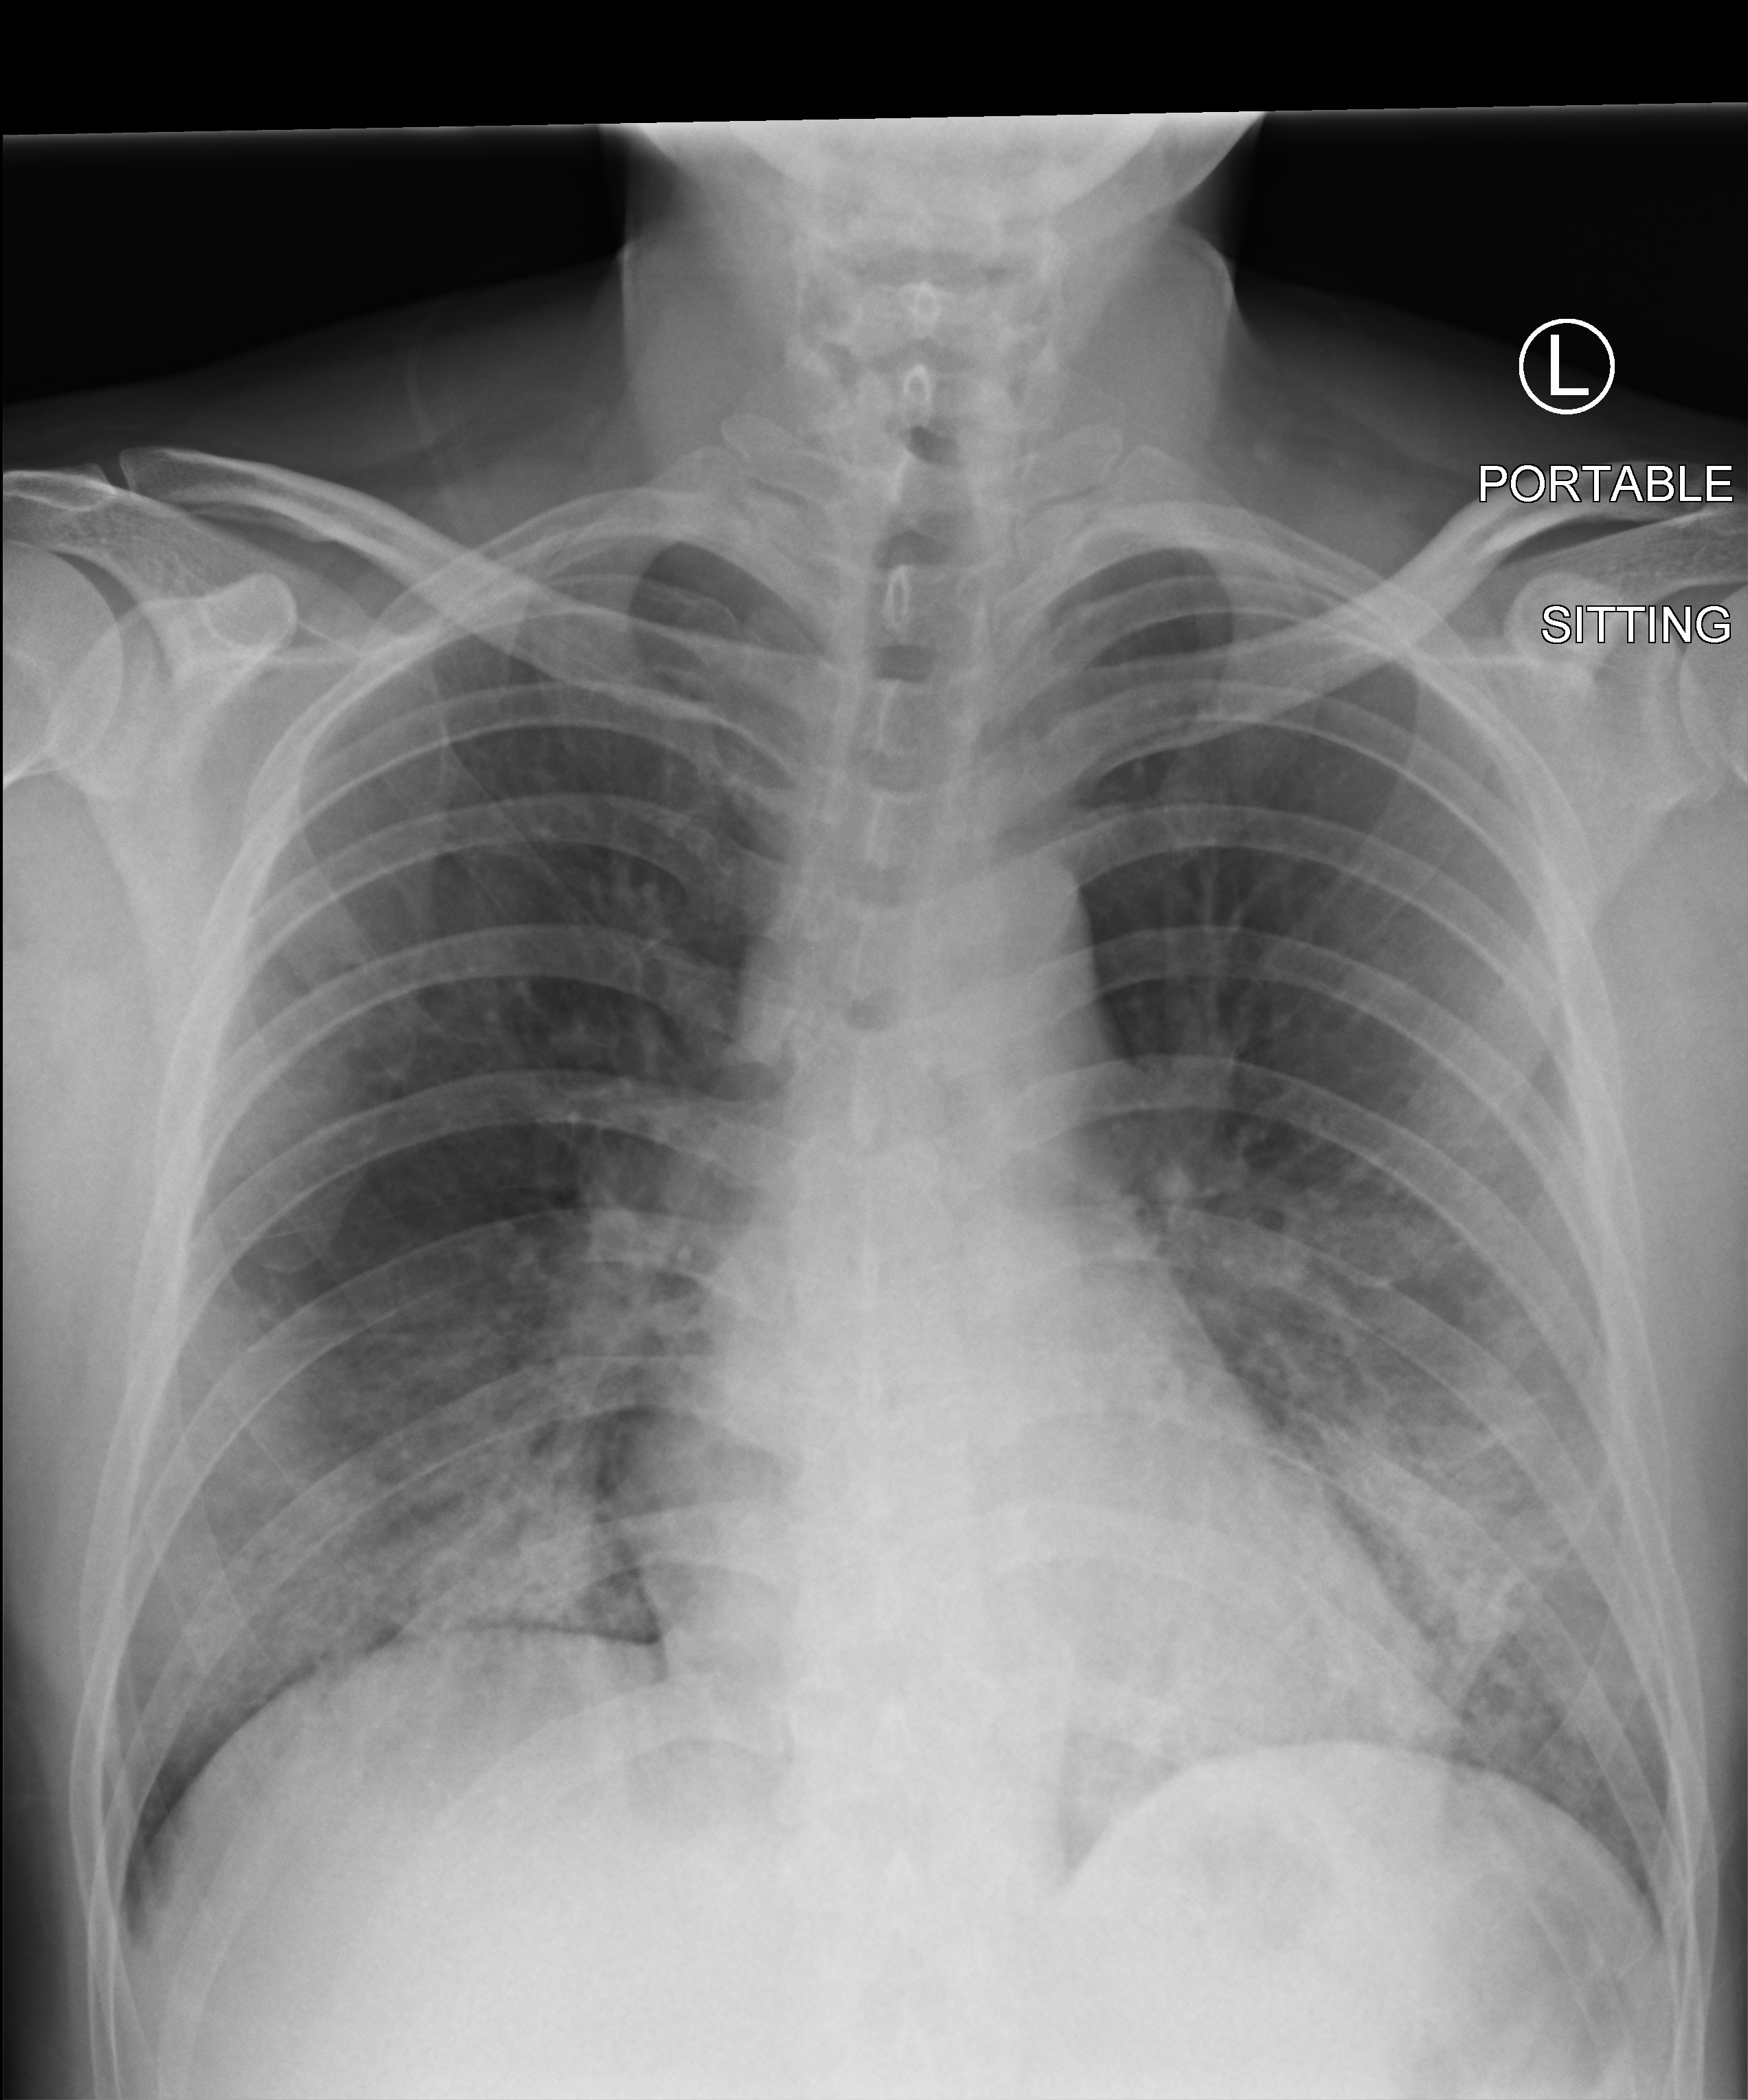
Chest X-ray (portable), anteroposterior (AP) projection. Patient hospitalised with COVID-19; male, aged 18–59 years.
From the hospital-stay record, not from the radiograph (when in the stay this image was taken is not recorded):
- mechanically ventilated during this hospital stay: no
- admitted to intensive care during this hospital stay: no